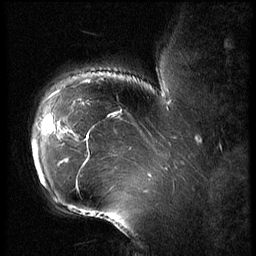
Breast MRI (dynamic contrast-enhanced), one sagittal slice; position 50 of 62 along the scan axis; 3 images stored at this slice position (order not interpretable as contrast timing); 1.5 T; TE 4.2 ms, TR 9 ms; 2.5 mm slice thickness; 256 × 256 image matrix, field of view 180 × 180 mm. Patient: female, 43 years. From the clinical record (not read from this slice): setting: breast cancer imaged before/during neoadjuvant chemotherapy; receptor status: HER2-positive.
Outlined on this slice (semi-automatic segmentation, software-assisted and operator-edited):
- analysis volume of interest (the breast-tissue region the enhancement analysis was run in; not a lesion): bounding box (x1, y1, x2, y2) in pixels: (29, 90, 82, 203)
- tumour enhancement mask (voxels above the 140 % enhancement threshold inside the analysis volume of interest): (33, 115, 78, 180)